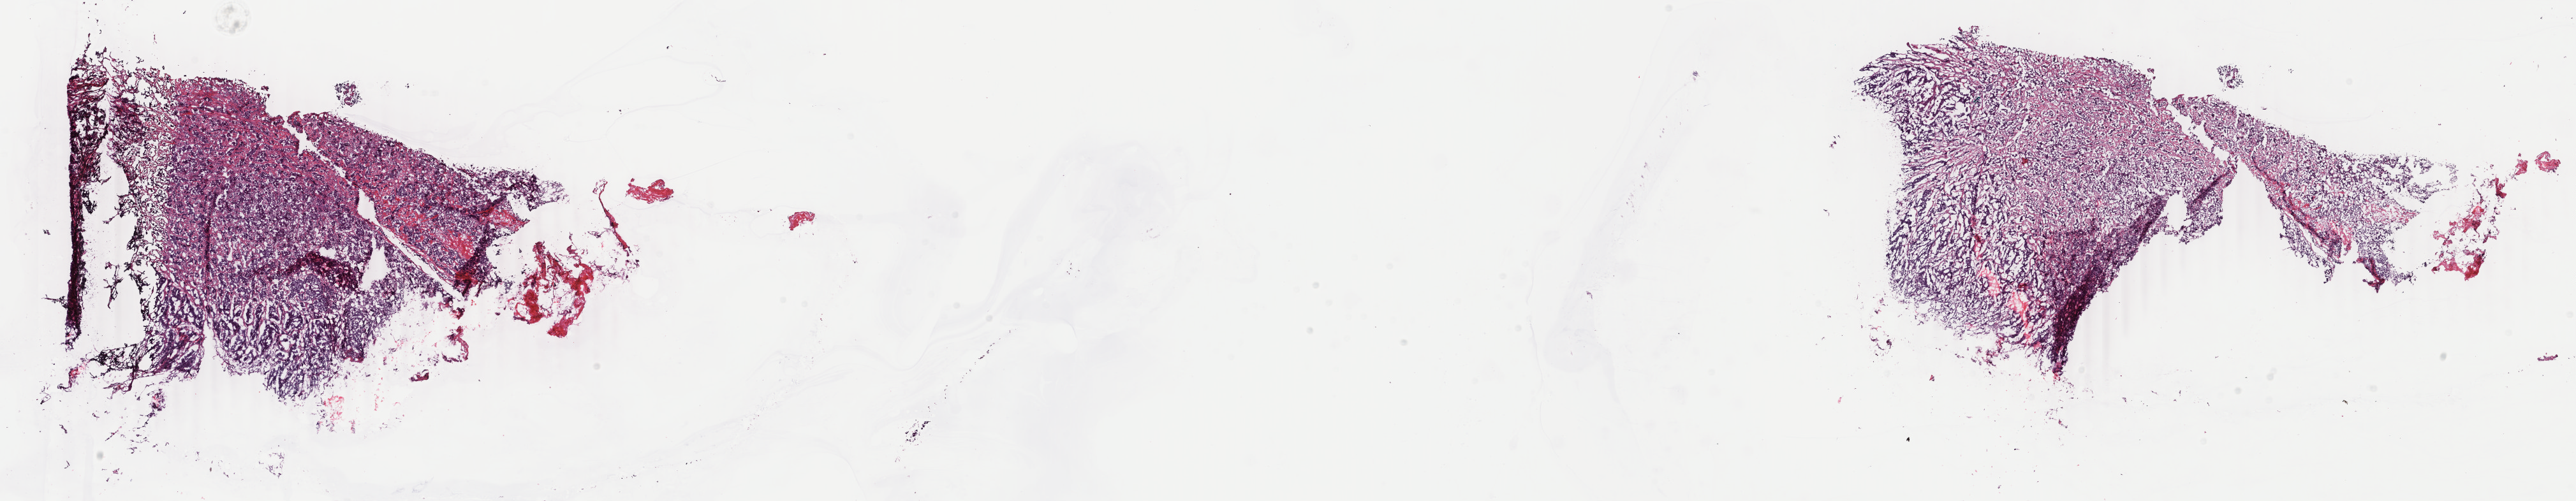
Hematoxylin and eosin (H&E) stained whole-slide image — shown as a low-resolution overview of the whole scanned area (about 32.1 x 6.3 mm); frozen section; sample: primary tumour, breast. Female, age 39 years at initial diagnosis. Slide review estimates, as recorded: tumour cells 90%, tumour nuclei 90%, normal cells 0%, stromal cells 10%, necrosis 0%. Inflammatory infiltration, as recorded: lymphocyte infiltration 0%, monocyte infiltration 0%, neutrophil infiltration 0%.
Pathologic diagnosis: Infiltrating duct carcinoma, NOS. AJCC pathologic stage: IIA (6th edition). Lymph nodes positive (case pathology): 0 of 2 examined. Laterality: right.